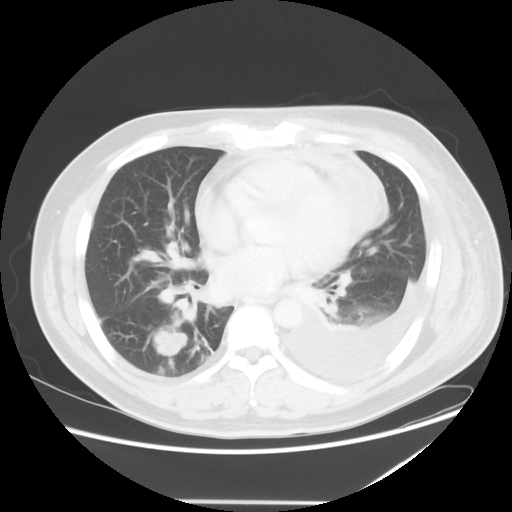
Chest CT, one axial slice. Slice 22 of 52 in the series (ordered by position). Reconstruction kernel STANDARD. 120 kVp. Lung window (W 1500 / L -600 HU). 5 mm slice thickness. 512 × 512 image matrix, field of view 405 × 405 mm. Patient: male, 42 years. From the clinical record (not read from this slice): clinical TNM (as recorded): T2 N1 M1.
Structures marked on this image (bounding box drawn by a radiologist):
- lung tumour (recorded histology: adenocarcinoma): bounding box <148,327,196,359> (left, top, right, bottom; pixels)